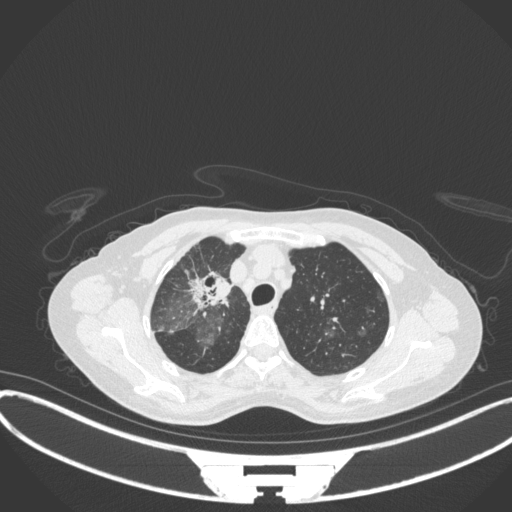
Chest CT, one axial slice; lung window (W 1500 / L -600 HU); 512 × 512 image matrix, field of view 400 × 400 mm. Female patient, age 59 years. Case-level facts recorded for this patient, not image findings: clinical TNM (as recorded): T3 N0 M0; histopathological grade: G1.
Outlined on this slice (rectangle marked by the reading radiologist):
- lung tumour (recorded histology: adenocarcinoma): bounding box (x1, y1, x2, y2) in pixels: (188, 270, 236, 315)